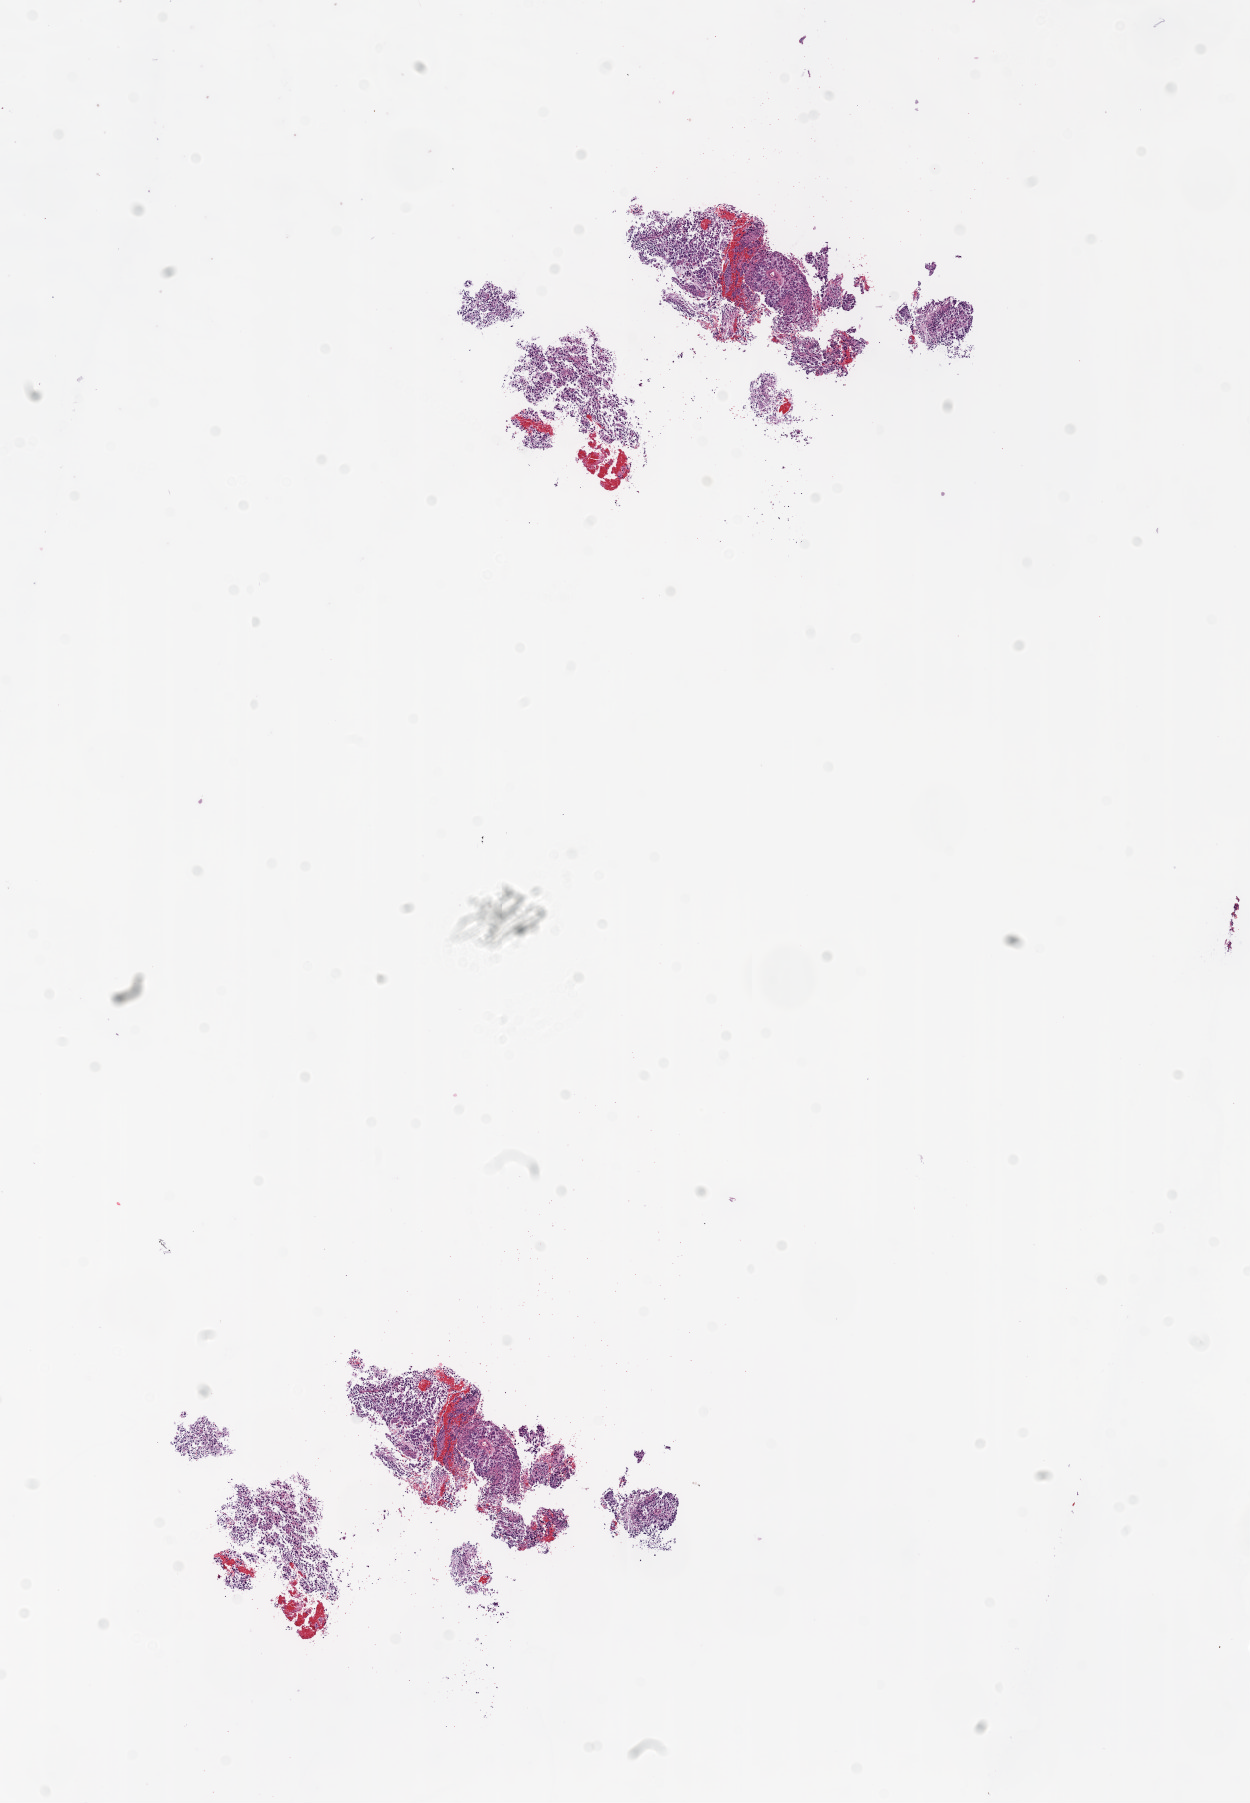
Whole-slide histology image, Hematoxylin and eosin (H&E) stained, low-resolution overview of the scanned area, about 10.0 x 14.5 mm. Formalin-fixed paraffin-embedded (FFPE) diagnostic section. Brain, primary tumour sample. Female patient; age at initial diagnosis 61 years.
Diagnosis: Glioblastoma.